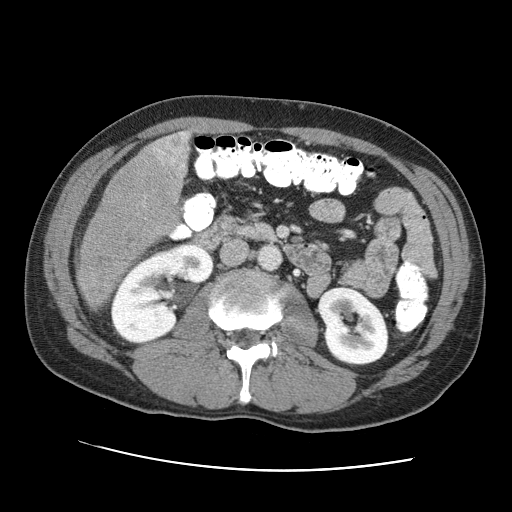
Contrast-enhanced abdominal CT (liver protocol), one axial slice; position 20 of 95 along the scan axis; one of 2 acquisitions stored at this slice position; soft-tissue window (W 400 / L 40 HU); 2.5 mm slice thickness; 512 × 512 image matrix. Case-level facts recorded for this patient, not image findings: diagnosis: hepatocellular carcinoma (patient treated with transarterial chemoembolisation; whether this scan precedes or follows treatment is not stated here); TNM stage (as recorded): Stage-IVA.
Annotated regions visible in this slice (semi-automatically segmented with operator editing):
- liver parenchyma outside the tumour (the mass and vessels are separate outlines, so this box may not span the whole liver): bounding box <76,130,190,287> (left, top, right, bottom; pixels)
- mass: <76,131,187,311>